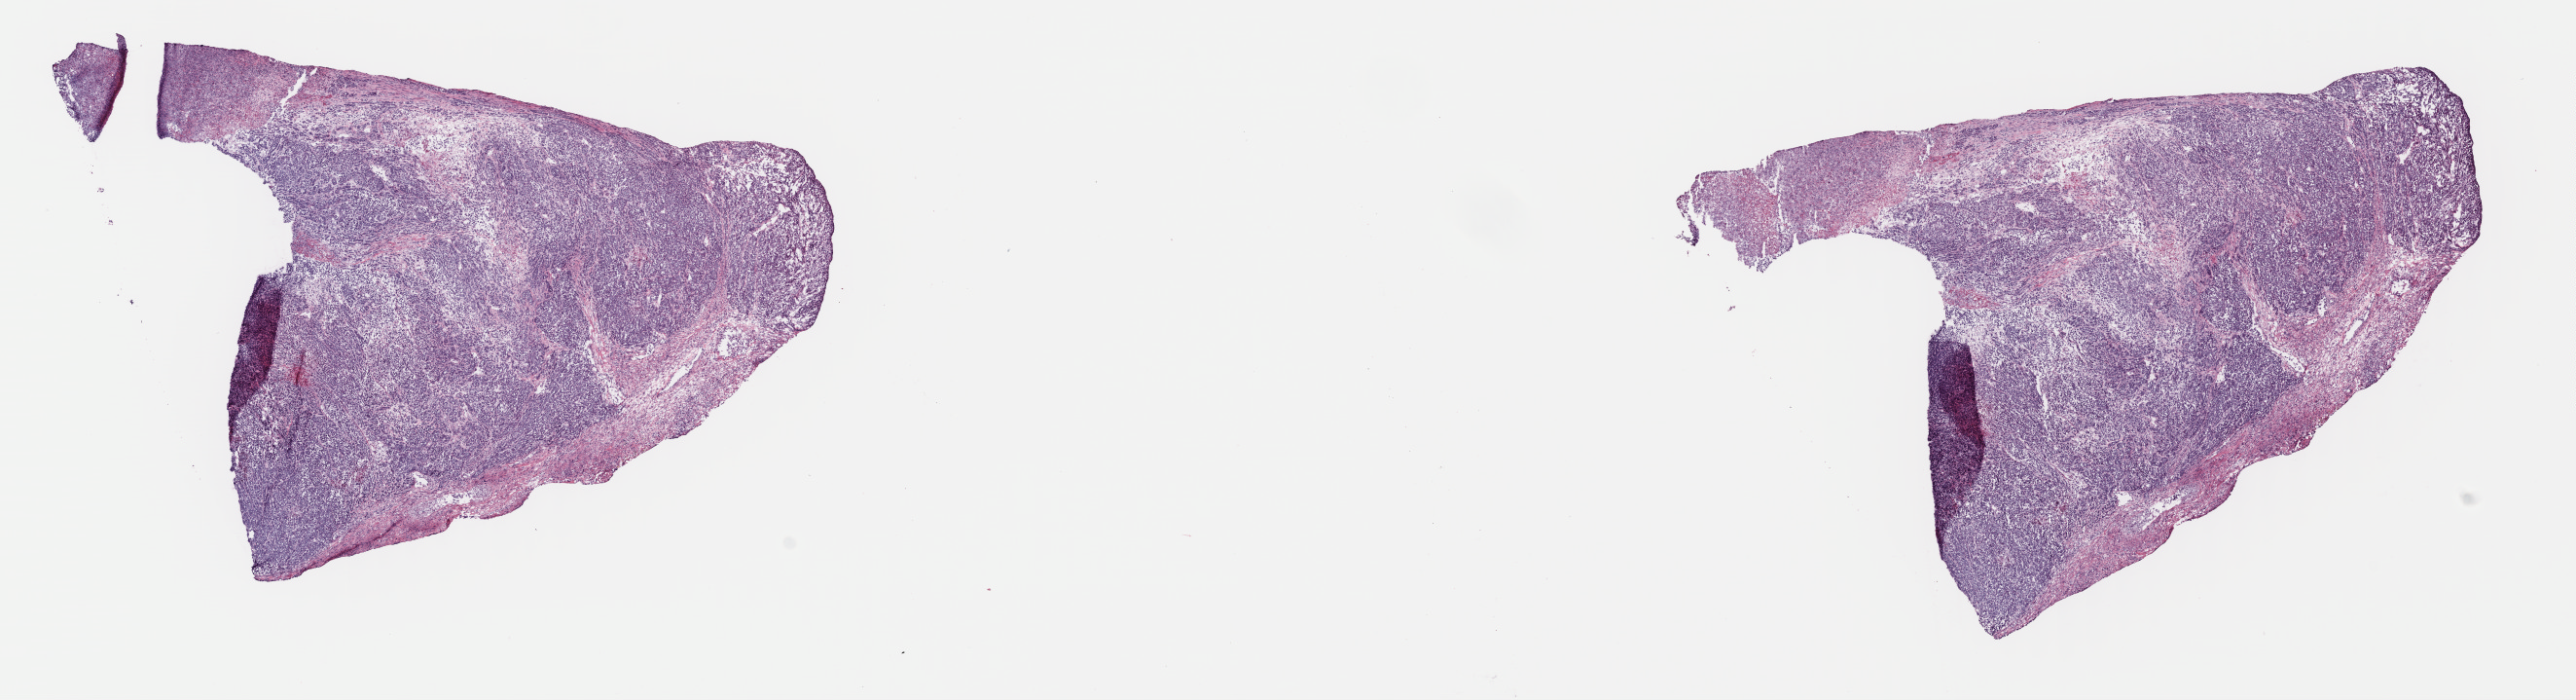
Whole-slide histology image, H&E-stained — low-resolution overview of the scanned area, about 20.8 x 5.7 mm, frozen section from the top of the tissue portion, primary tumour sample from the skin. Male, age 39 years at initial diagnosis. Pathologist review of this section (percent, as recorded): tumour cells 65%, tumour nuclei 80%, normal cells 0%, stromal cells 20%, necrosis 15%. Infiltration values recorded for this section: lymphocyte infiltration 2%, monocyte infiltration 3%, neutrophil infiltration 0%.
AJCC pathologic stage: IIC (7th edition). Diagnosis: Nodular melanoma.